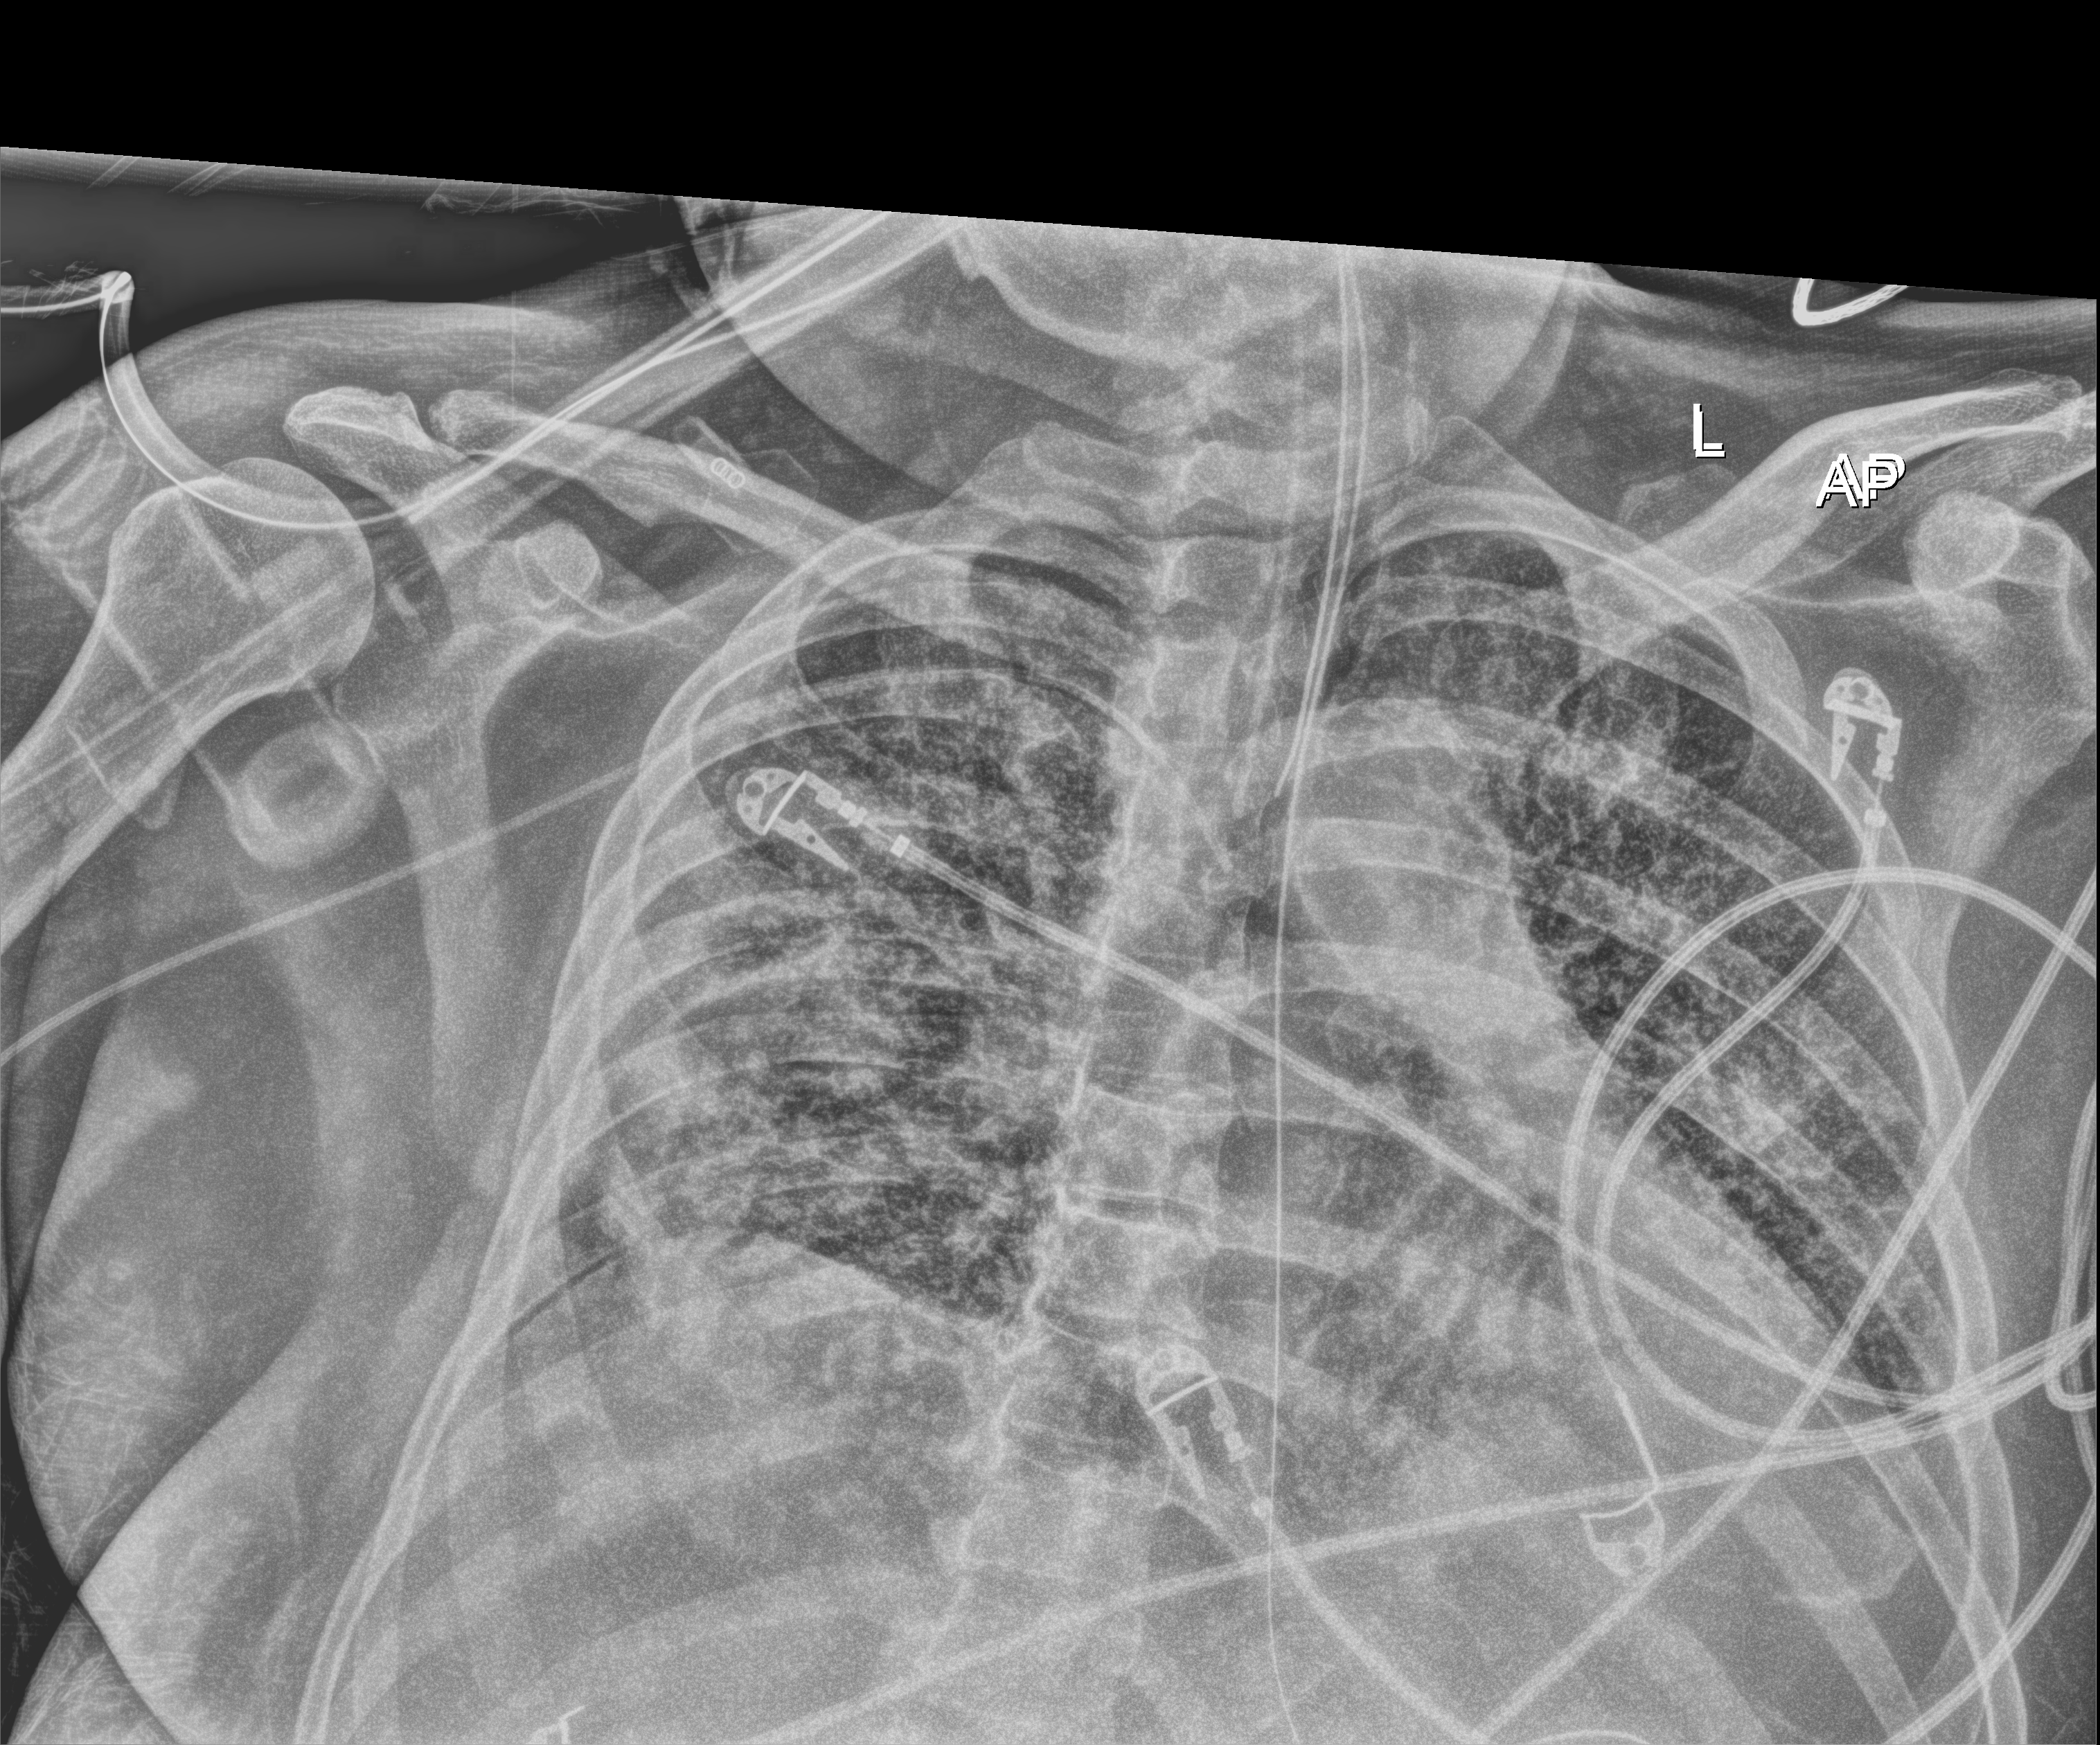
Chest X-ray (portable); anteroposterior (AP) projection. Patient hospitalised with COVID-19; male, aged 18–59 years.
From the hospital-stay record, not from the radiograph (when in the stay this image was taken is not recorded): smoking status (admission record): never.